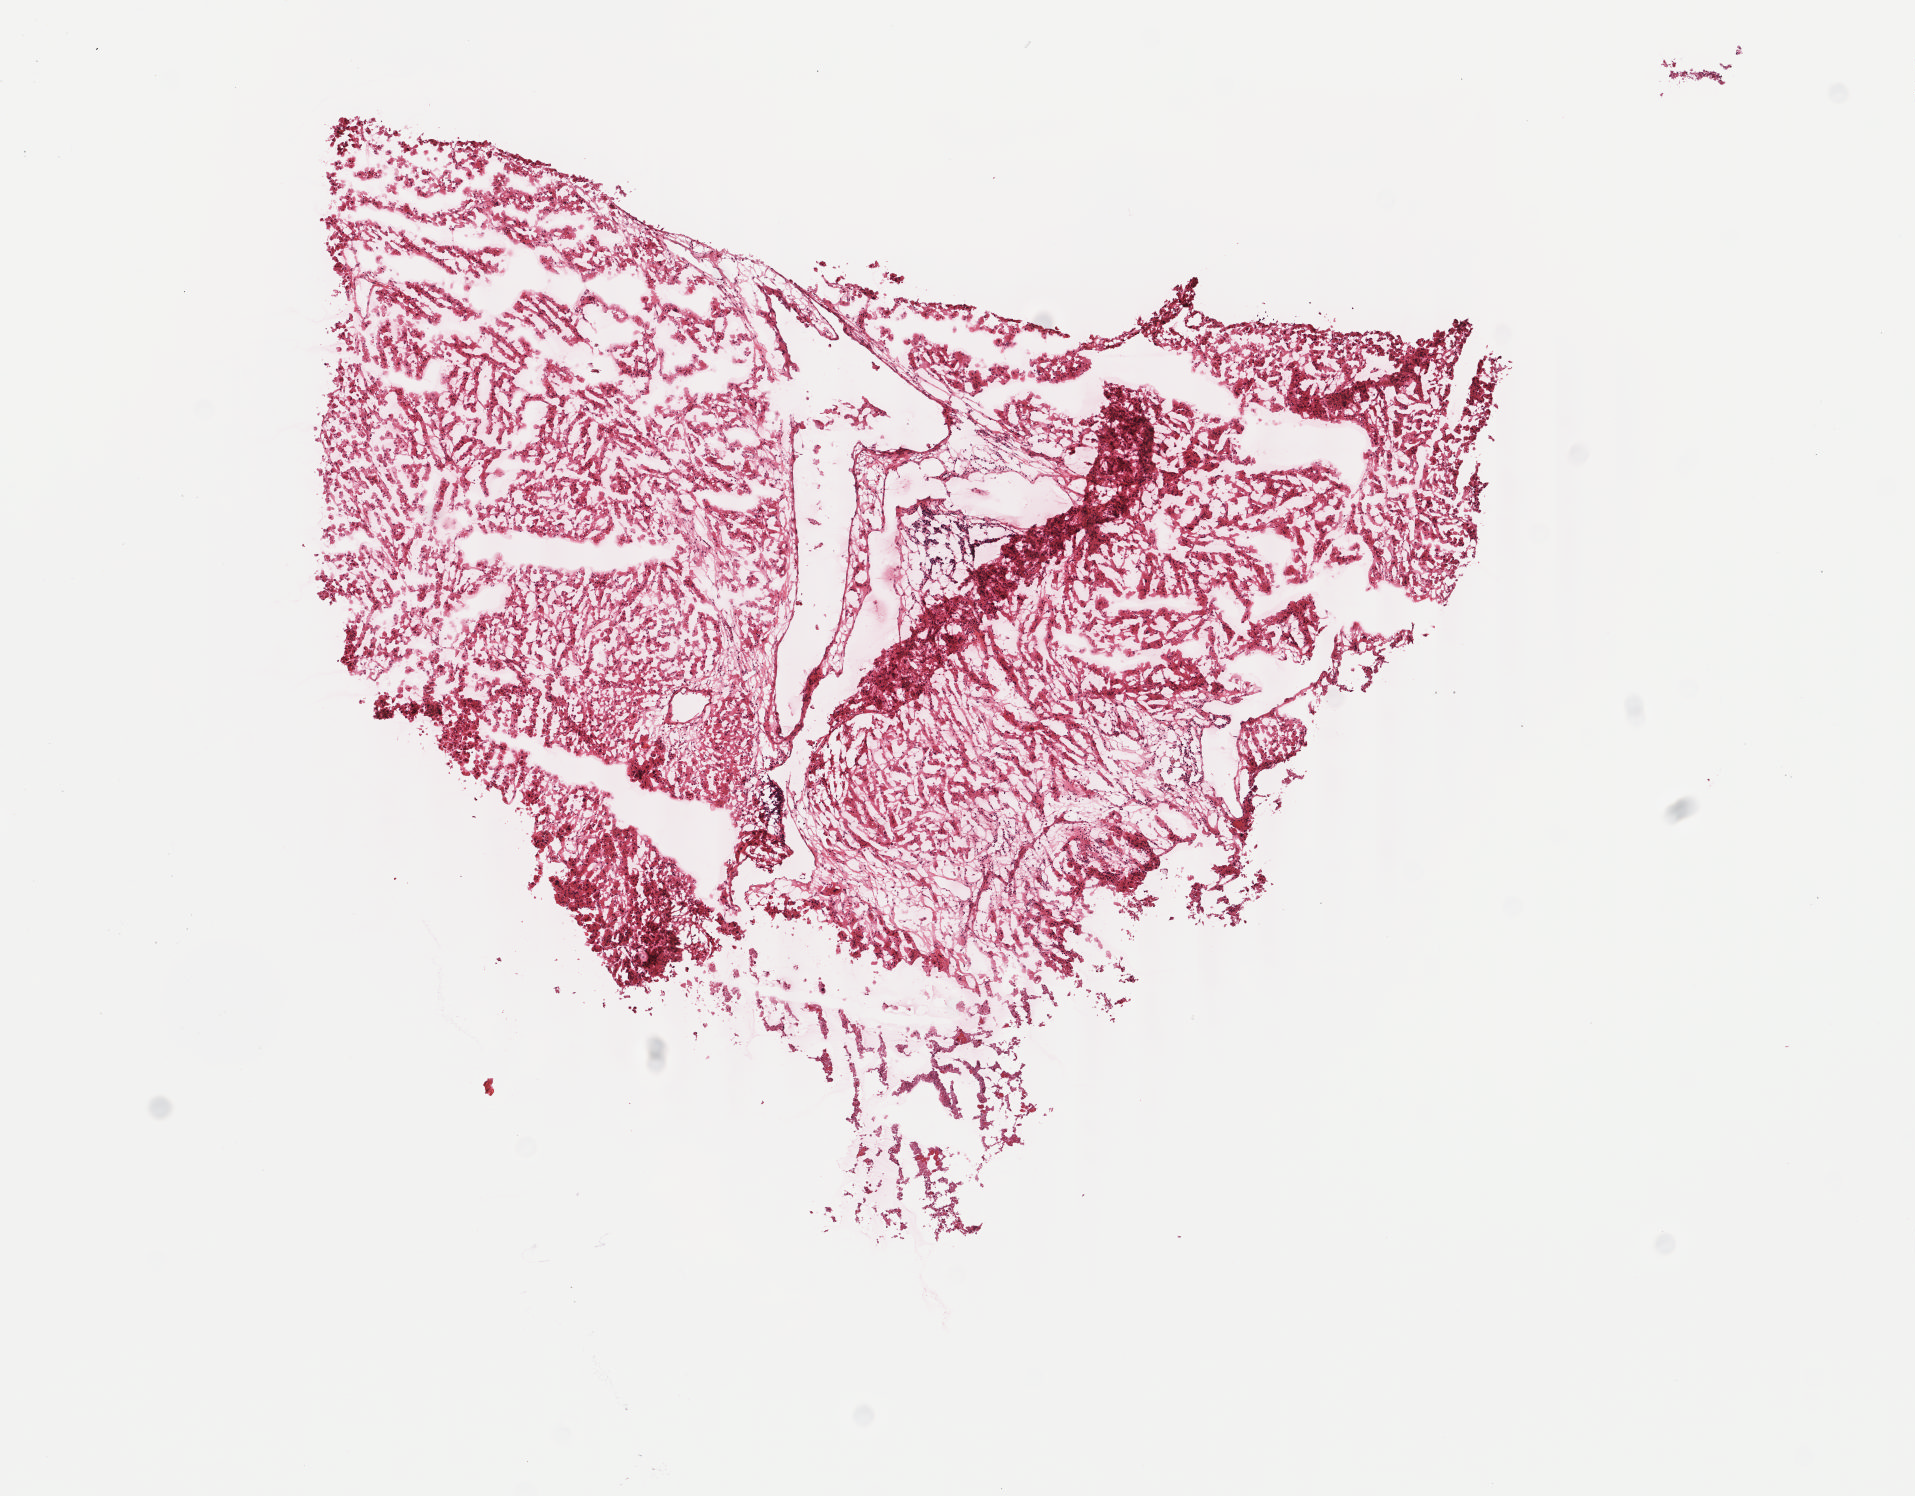
H&E whole-slide image — whole scanned area (about 7.6 x 5.9 mm) shown as a low-resolution overview, frozen section from the top of the tissue portion, sample: primary tumour, adrenal cortex. Female, age 32 years at initial diagnosis. Composition of this section per pathologist review: tumour cells 95%, tumour nuclei 90%.
Diagnosis: Adrenal cortical carcinoma (cortex of adrenal gland).